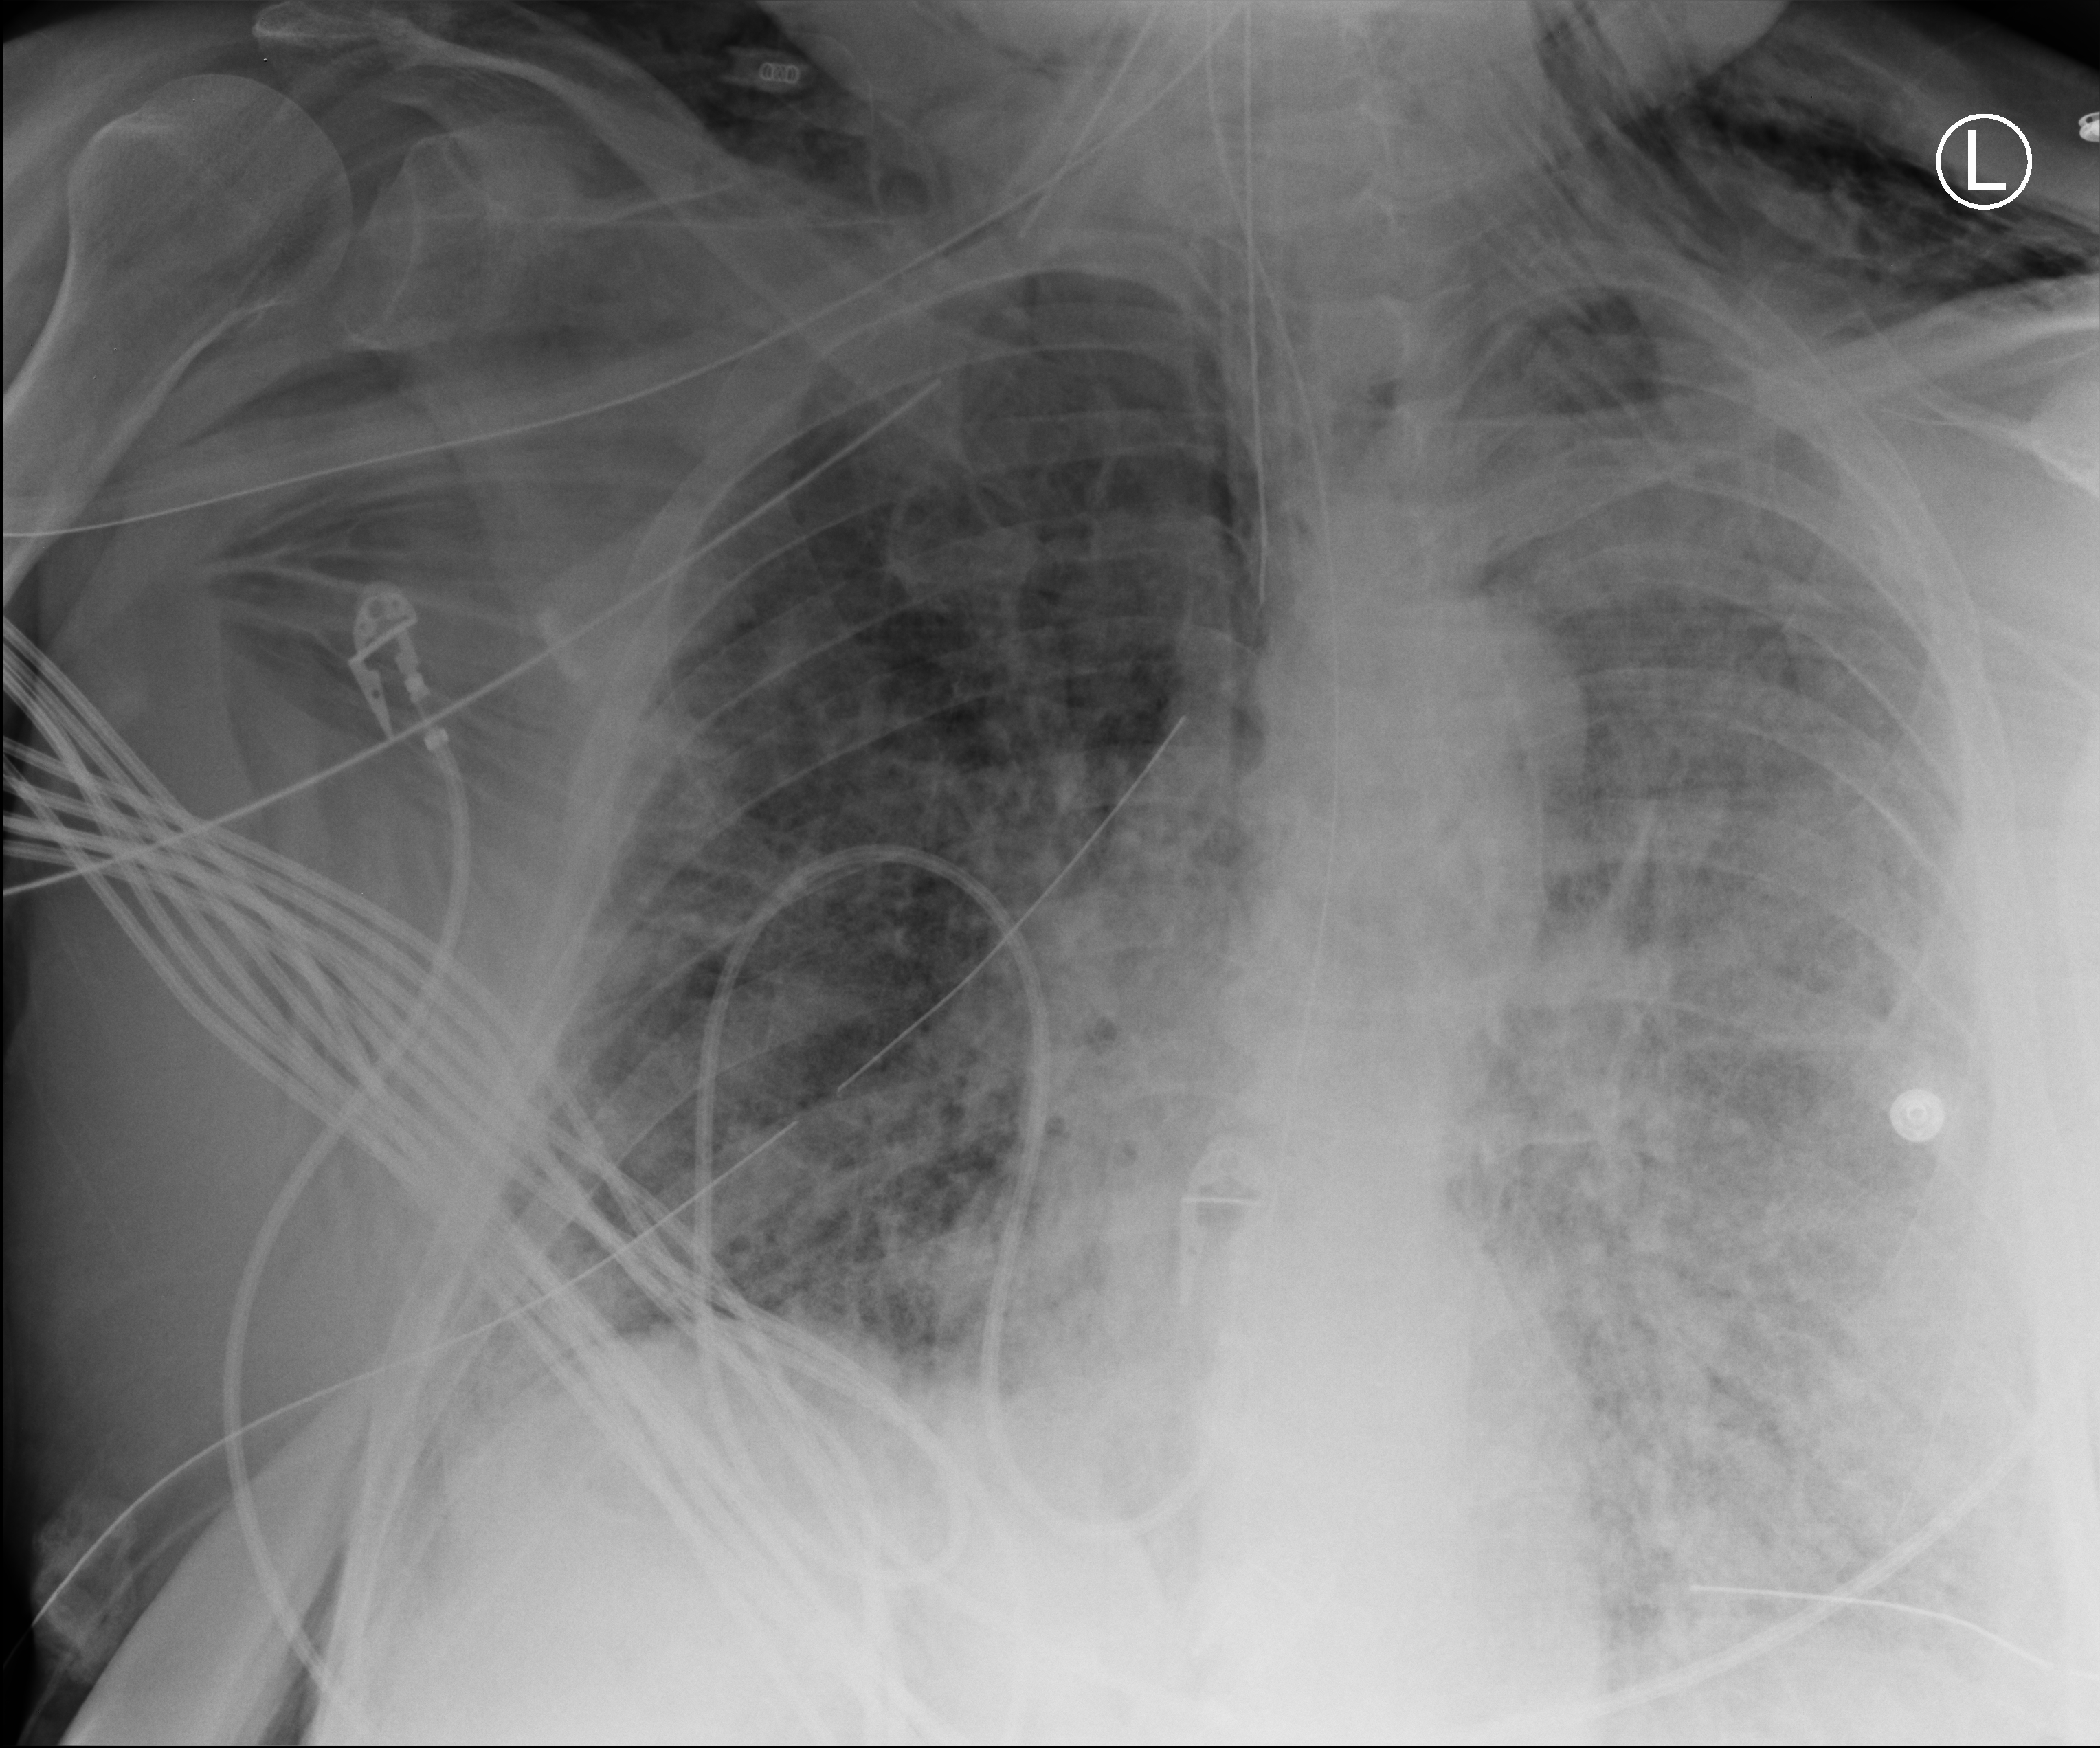
Portable chest radiograph, anteroposterior (AP) projection. Patient hospitalised with COVID-19, aged 18–59 years.
Hospital-stay facts (about this admission, not read from this image; timing relative to this image not recorded): diabetes (admission record): no.